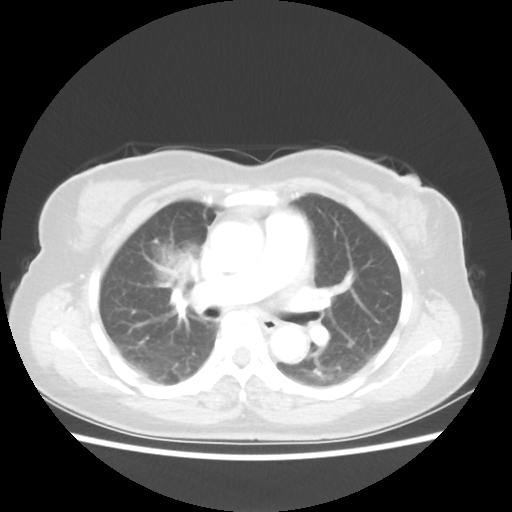
Chest CT, one axial slice. Position 32 of 55 along the scan axis. 80 kVp. Lung window (W 1500 / L -600 HU). 5 mm slice thickness. 512 × 512 image matrix, field of view 337 × 337 mm. Patient: female, 62 years. From the clinical record (not read from this slice): clinical TNM (as recorded): T4 N3 M0.
Annotated regions visible in this slice (bounding box drawn by a radiologist):
- lung tumour (recorded histology: squamous cell carcinoma): bounding box [x1, y1, x2, y2] px = [143, 234, 212, 301]